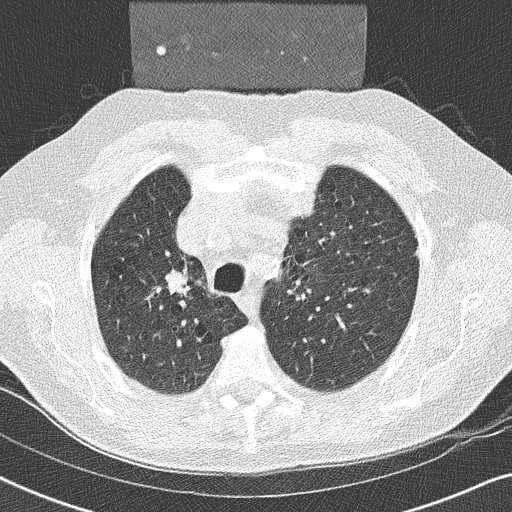
Low-dose screening chest CT, one axial slice; position 183 of 252 along the scan axis; reconstruction kernel B50f; 120 kVp; lung window (W 1500 / L -600 HU); 2 mm slice thickness; 512 × 512 image matrix, field of view 330 × 330 mm.
Outlined on this slice (manually delineated by an expert):
- lesion 1 (tumor, upper lobe of right lung): bounding box (x1, y1, x2, y2) in pixels: (166, 270, 187, 293)